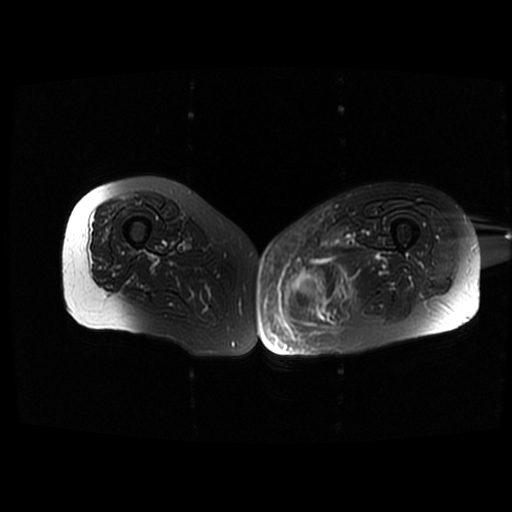
MRI of an extremity soft-tissue mass, one axial slice; slice 41 of 42 in the series (ordered by position); T2-weighted fat-saturated; 6 mm slice thickness; 512 × 512 image matrix, field of view 420 × 420 mm. Female patient. Case-level facts recorded for this patient, not image findings: histological type: pleomorphic leiomyosarcoma; grade: high; site of the primary tumour: left thigh.
Structures marked on this image (expert manual segmentation):
- gross tumour volume including surrounding oedema: bounding box <287,264,354,304> (left, top, right, bottom; pixels)